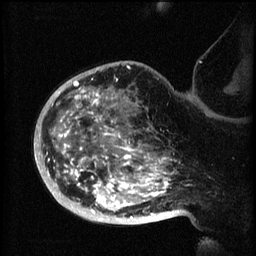
Breast MRI (dynamic contrast-enhanced), one sagittal slice. Position 46 of 60 along the scan axis. 3 images stored at this slice position (order not interpretable as contrast timing). 1.5 T. TE 4.2 ms, TR 8.2 ms. 2 mm slice thickness. 256 × 256 image matrix, field of view 200 × 200 mm. Female patient, age 50 years.
Structures marked on this image (semi-automatic segmentation, software-assisted and operator-edited):
- analysis volume of interest (the breast-tissue region the enhancement analysis was run in; not a lesion): box from (x=44, y=72) to (x=173, y=219) px
- tumour enhancement mask (voxels above the 70 % enhancement threshold inside the analysis volume of interest): (x=48, y=82)–(x=173, y=219)